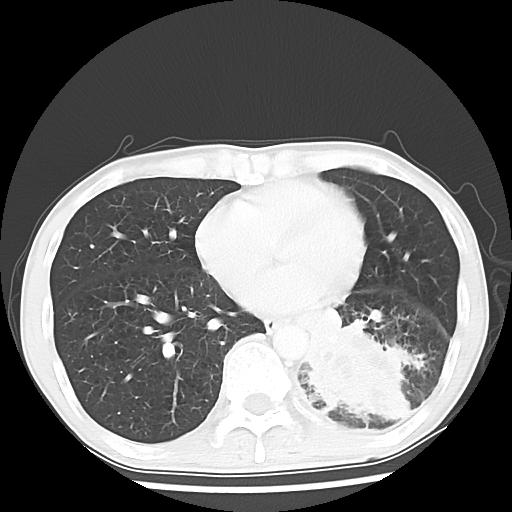
Chest CT, one axial slice. Slice 23 of 64 in the series (ordered by position). Reconstruction kernel LUNG. Lung window (W 1500 / L -600 HU). 512 × 512 image matrix. Patient: male, 68 years. From the clinical record (not read from this slice): clinical TNM (as recorded): T4 N0 M0.
Structures marked on this image (bounding box drawn by a radiologist):
- lung tumour (recorded histology: squamous cell carcinoma): bounding box [x1, y1, x2, y2] px = [297, 312, 425, 433]